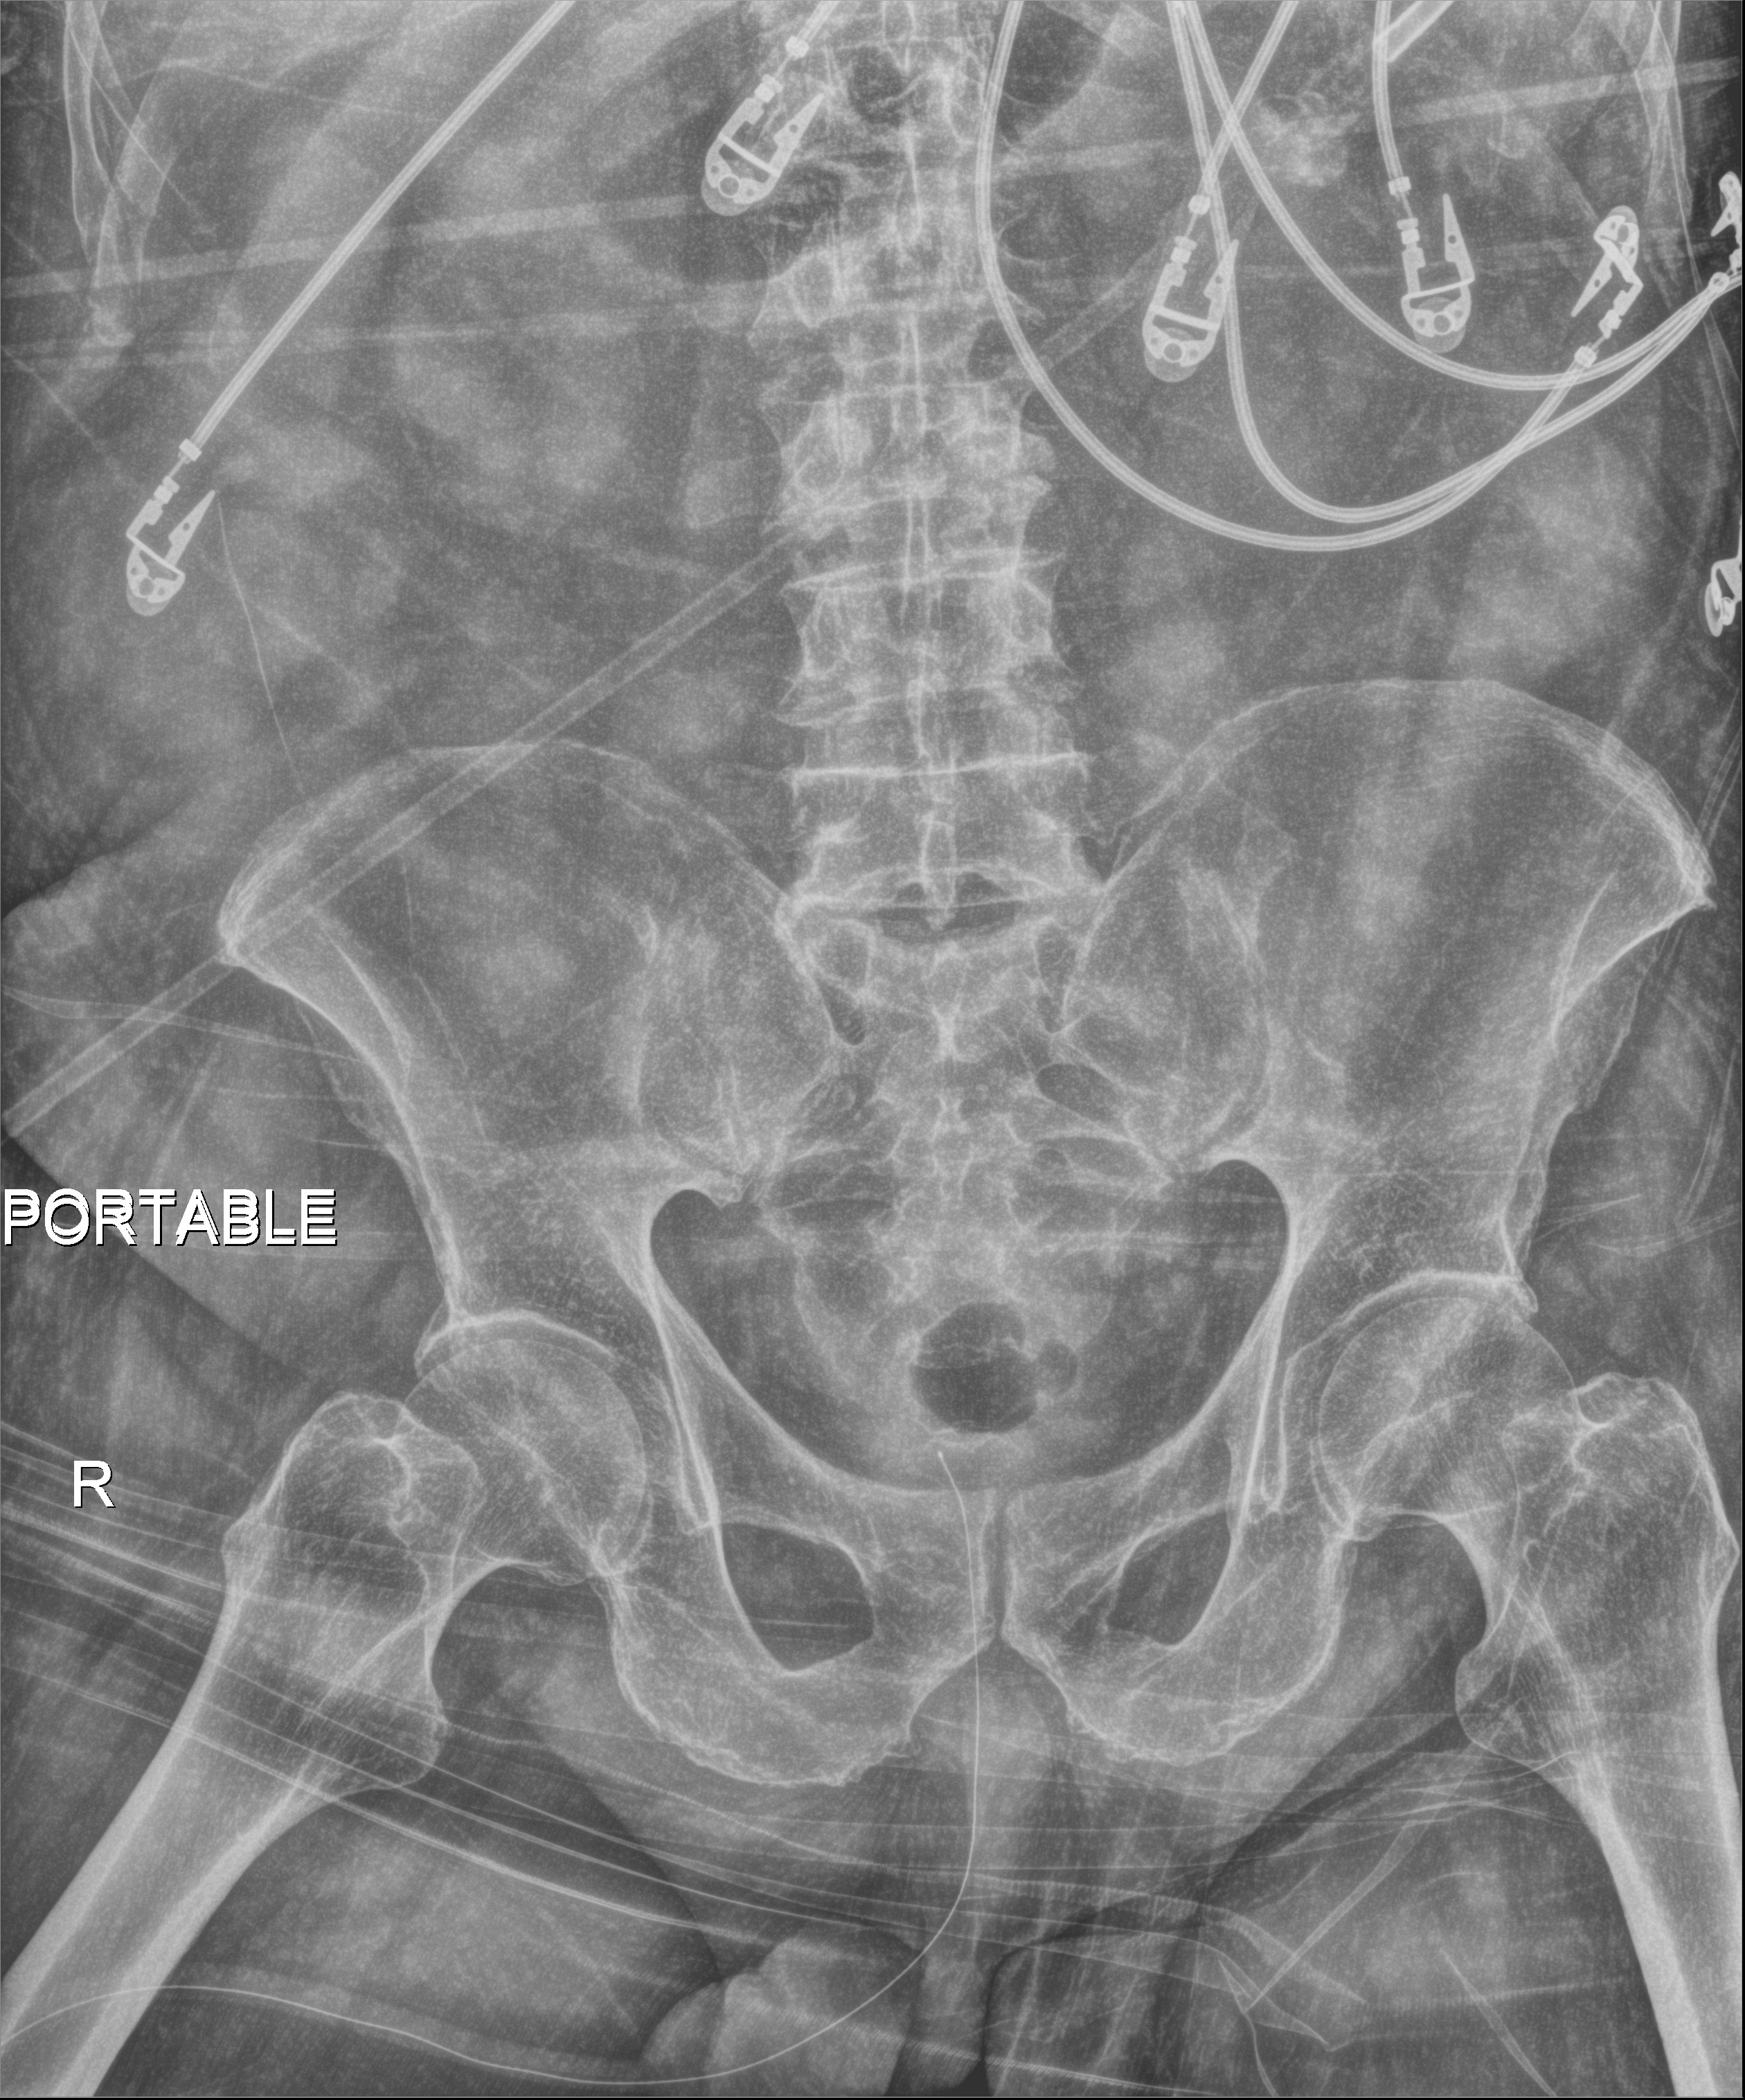
Bedside abdomen radiograph (digital radiography); anteroposterior (AP) projection. Male patient hospitalised with COVID-19, age 75–90 years.
Hospital-stay facts (about this admission, not read from this image; timing relative to this image not recorded): COPD (admission record): no; admitted to intensive care during this hospital stay: yes.